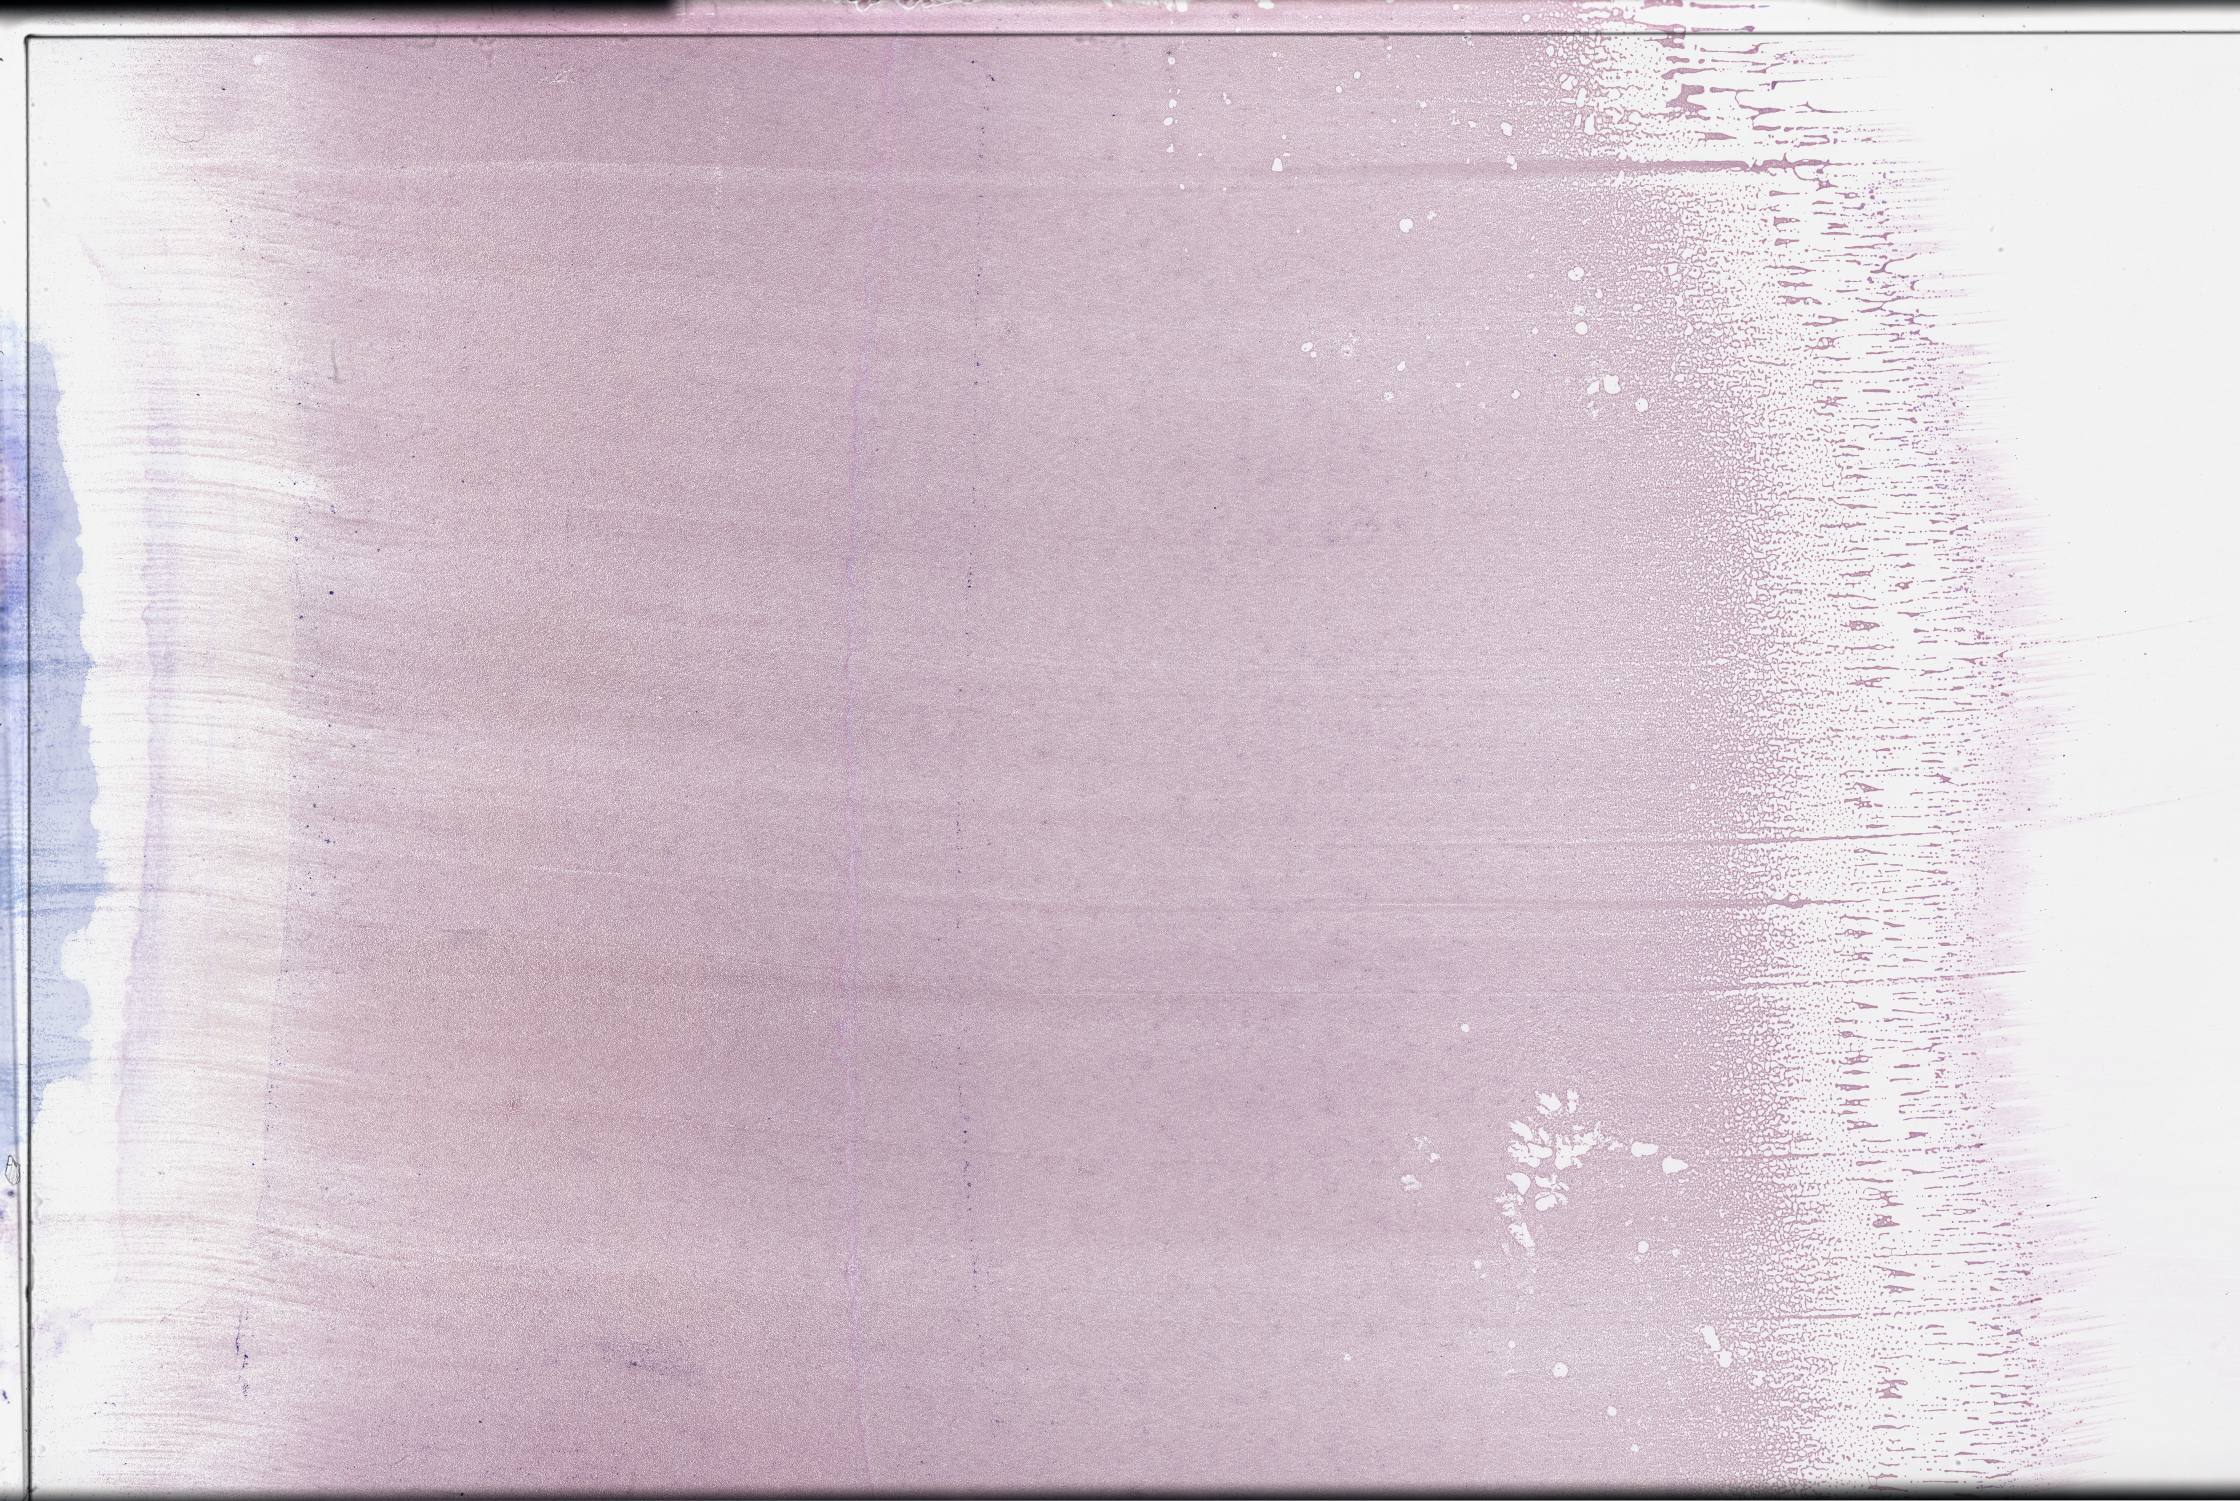
Whole-slide histology image, Hematoxylin and eosin (H&E) stained — a low-resolution overview of the entire scanned area, about 36.2 x 24.2 mm, peripheral blood (leukaemic) sample. 41-year-old female patient.
Diagnosis: Acute Myeloid Leukemia.